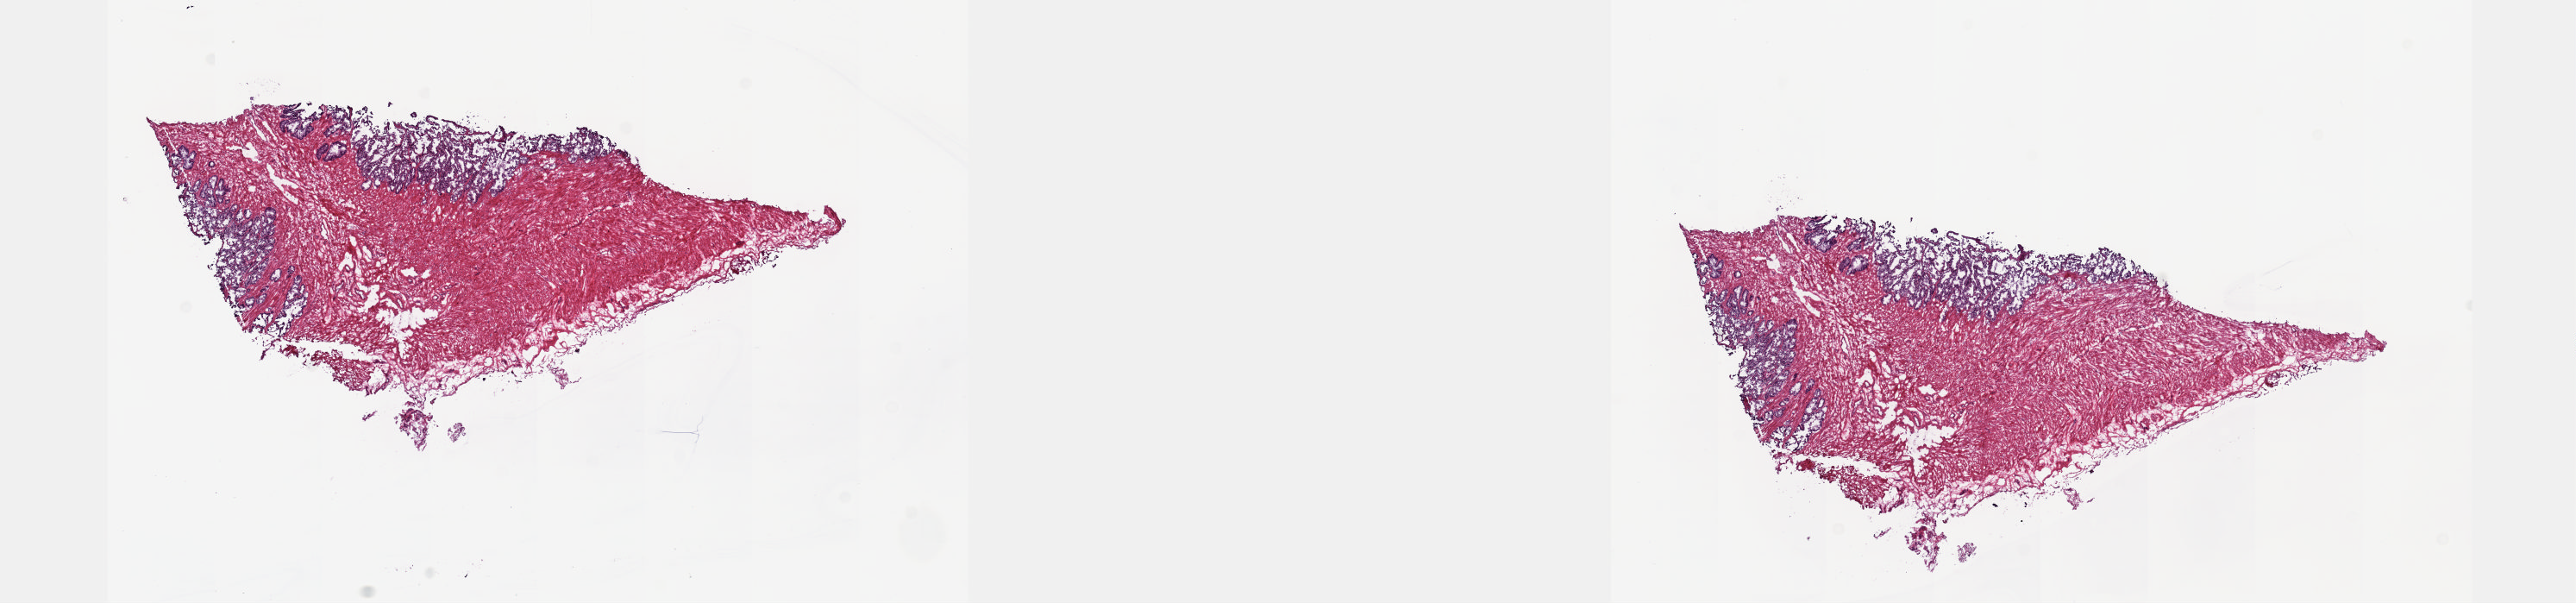
H&E whole-slide image — shown as a low-resolution overview of the whole scanned area (about 24.1 x 5.6 mm, slide scanned at 20x), frozen section, sample: solid tissue normal (non-tumour tissue), prostate. Male, age 54 years at initial diagnosis. Slide review estimates, as recorded: tumour cells 0%, tumour nuclei 0%, normal cells 100%, stromal cells 0%, necrosis 0%. Inflammatory infiltration, as recorded: lymphocyte infiltration 0%, monocyte infiltration 0%, neutrophil infiltration 0%.
* this section: solid tissue normal sample (biorepository sample class)
* patient diagnosis: Adenocarcinoma, NOS